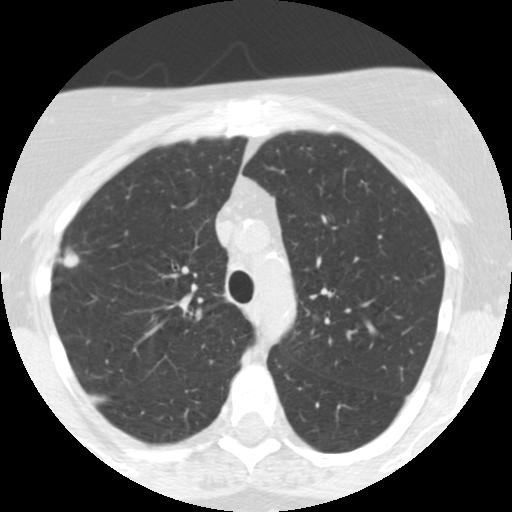
Low-dose screening chest CT, one axial slice. Slice 182 of 248 in the series (ordered by position). Reconstruction kernel STANDARD. 120 kVp. Lung window (W 1500 / L -600 HU). 2.5 mm slice thickness. 512 × 512 image matrix.
Structures marked on this image (outlined manually by an expert reader):
- lesion 1 (tumor, upper lobe of right lung): bounding box (x1, y1, x2, y2) in pixels: (58, 248, 80, 268)